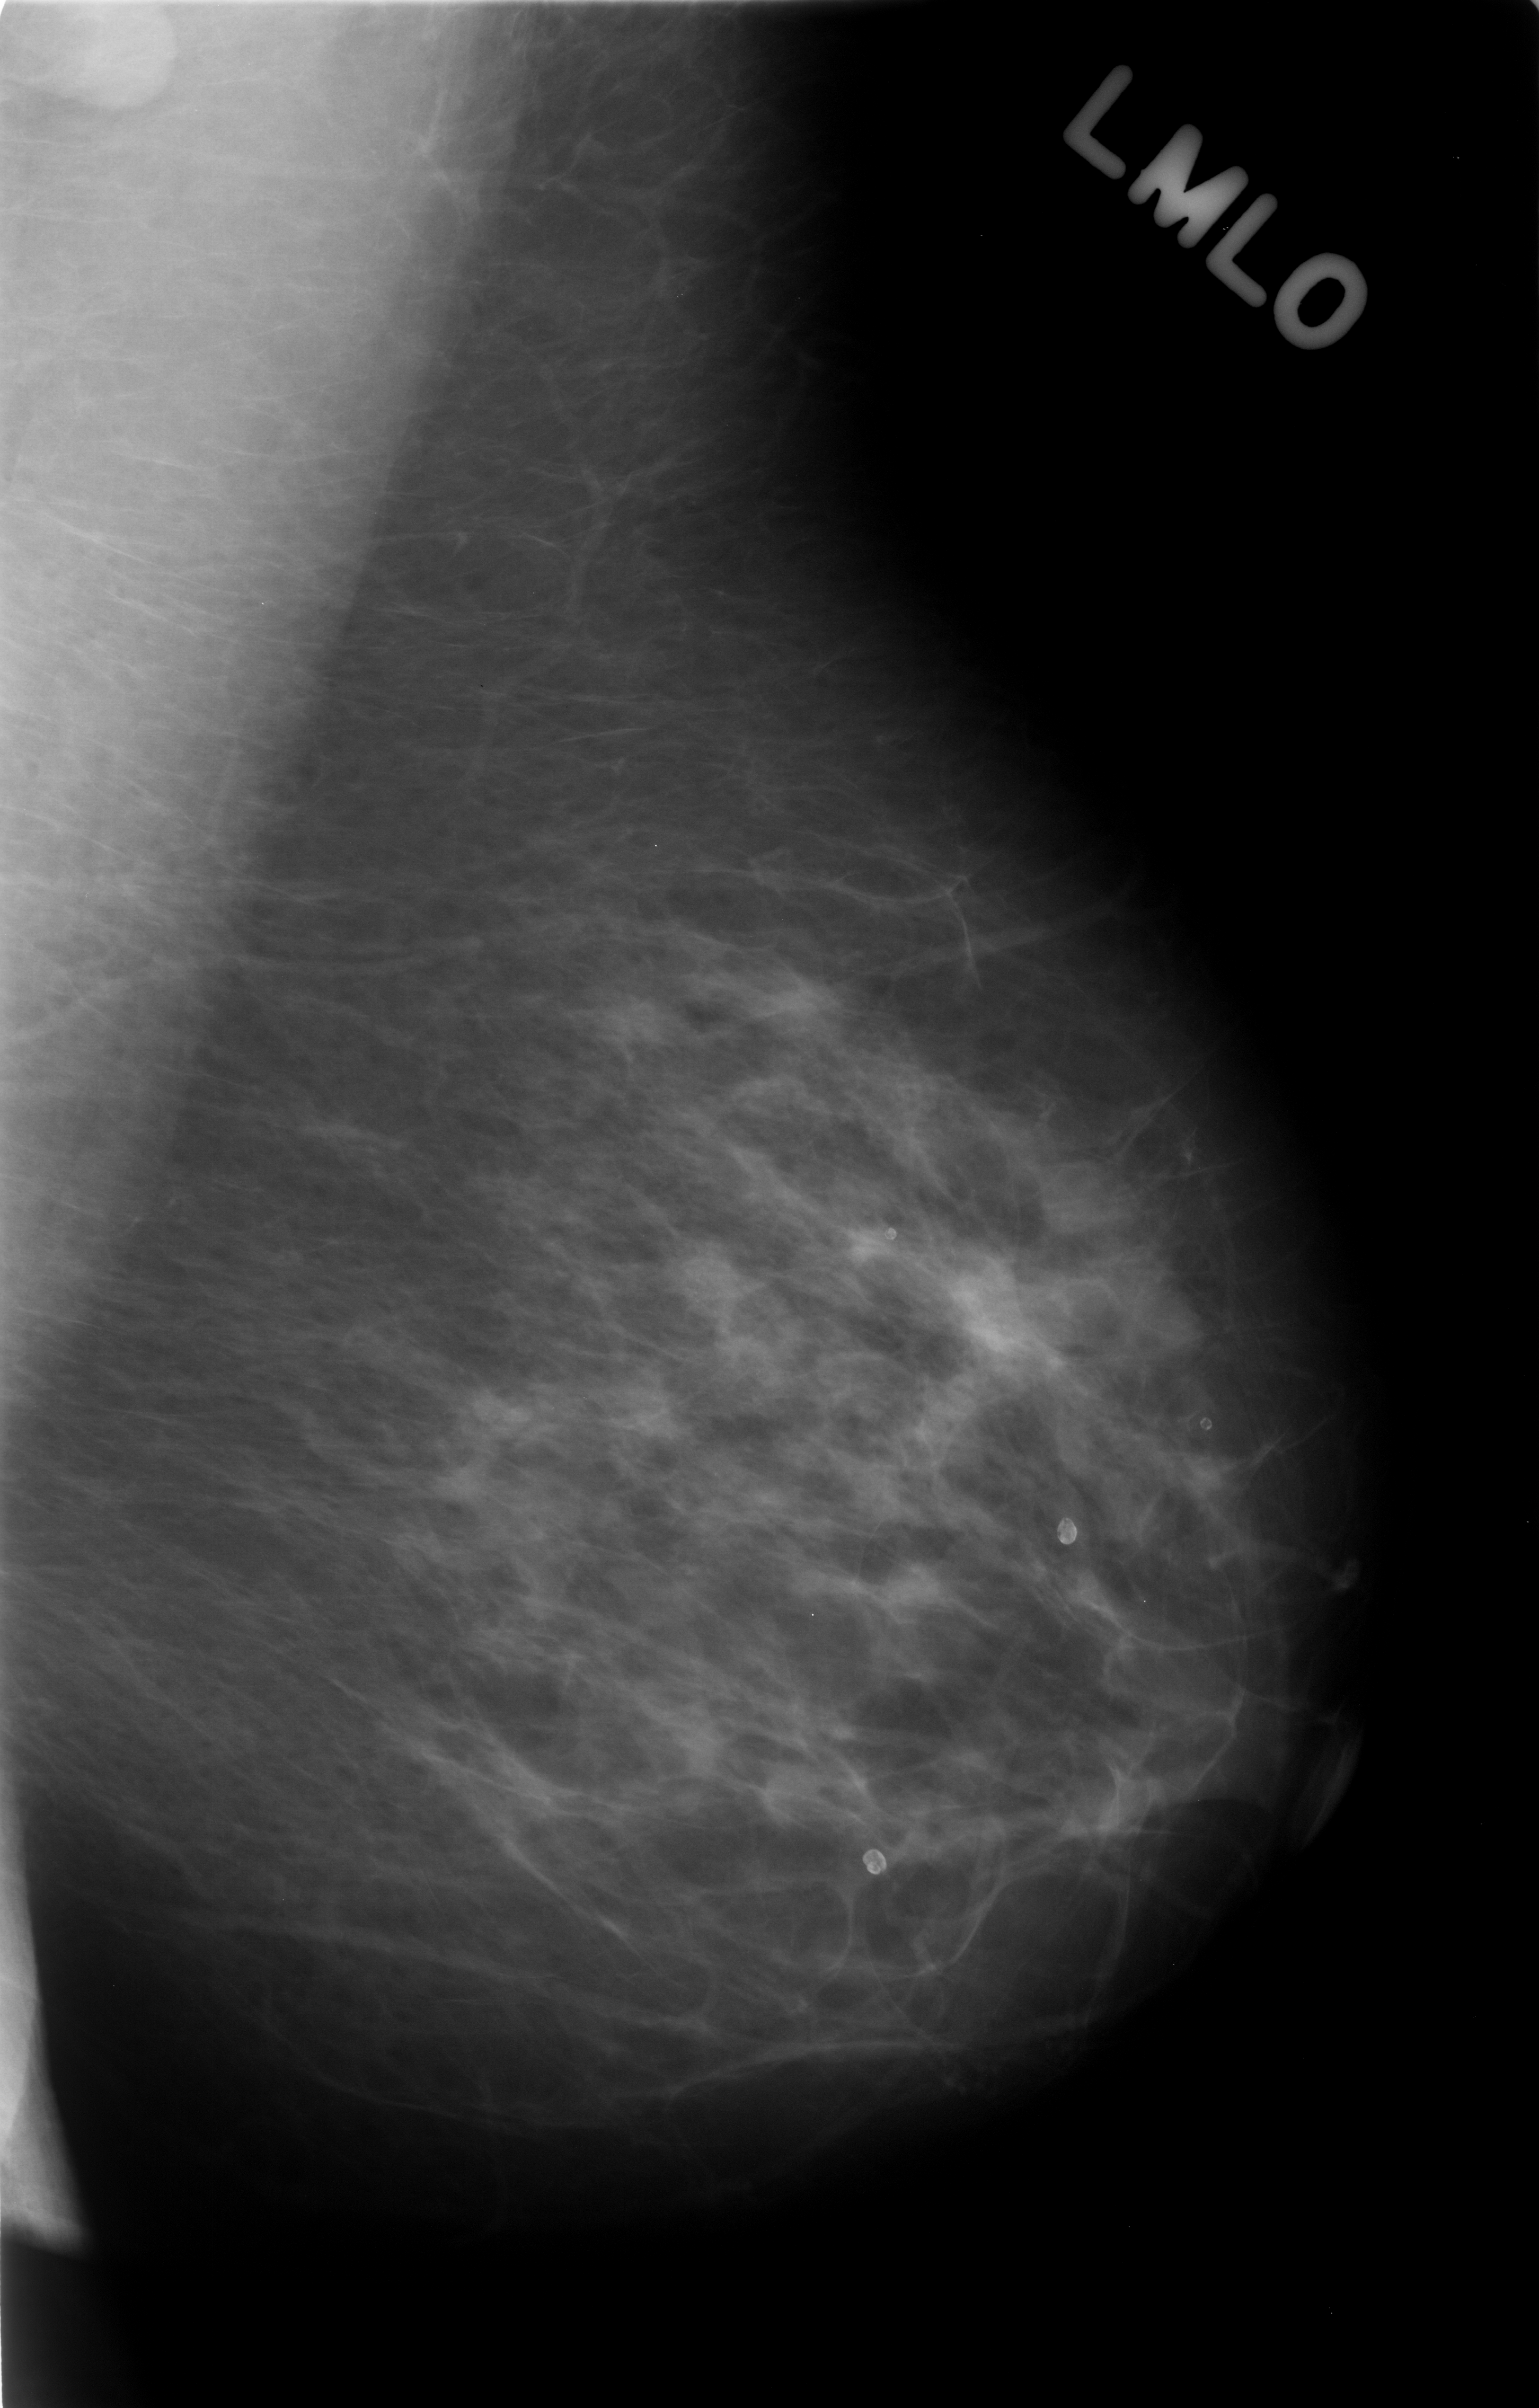
Scanned film-screen mammogram; left breast; mediolateral oblique (MLO) view; breast composition: scattered fibroglandular densities (BI-RADS density category 2 of 4).
- Finding: calcifications, morphology amorphous, distribution clustered; BI-RADS assessment category 4; subtlety rating 1 on a 1 (subtle) to 5 (obvious) scale; pathology result (as recorded, not read from the image): benign.